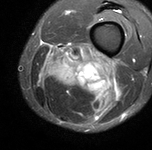
MRI of an extremity soft-tissue mass, one axial slice. Position 25 of 90 along the scan axis. STIR. MR volume resampled by the dataset authors to the PET/CT grid (not the native acquisition matrix). 3.27 mm slice thickness. 152 × 150 image matrix, field of view 148 × 146 mm. Male patient. Case-level facts recorded for this patient, not image findings: histological type: undifferentiated pleomorphic liposarcoma; grade: high; site of the primary tumour: left thigh.
Structures marked on this image (expert contour drawn on MRI and transferred to this co-registered scan by the dataset authors):
- gross tumour volume including surrounding oedema: bounding box (x1, y1, x2, y2) in pixels: (39, 43, 126, 115)